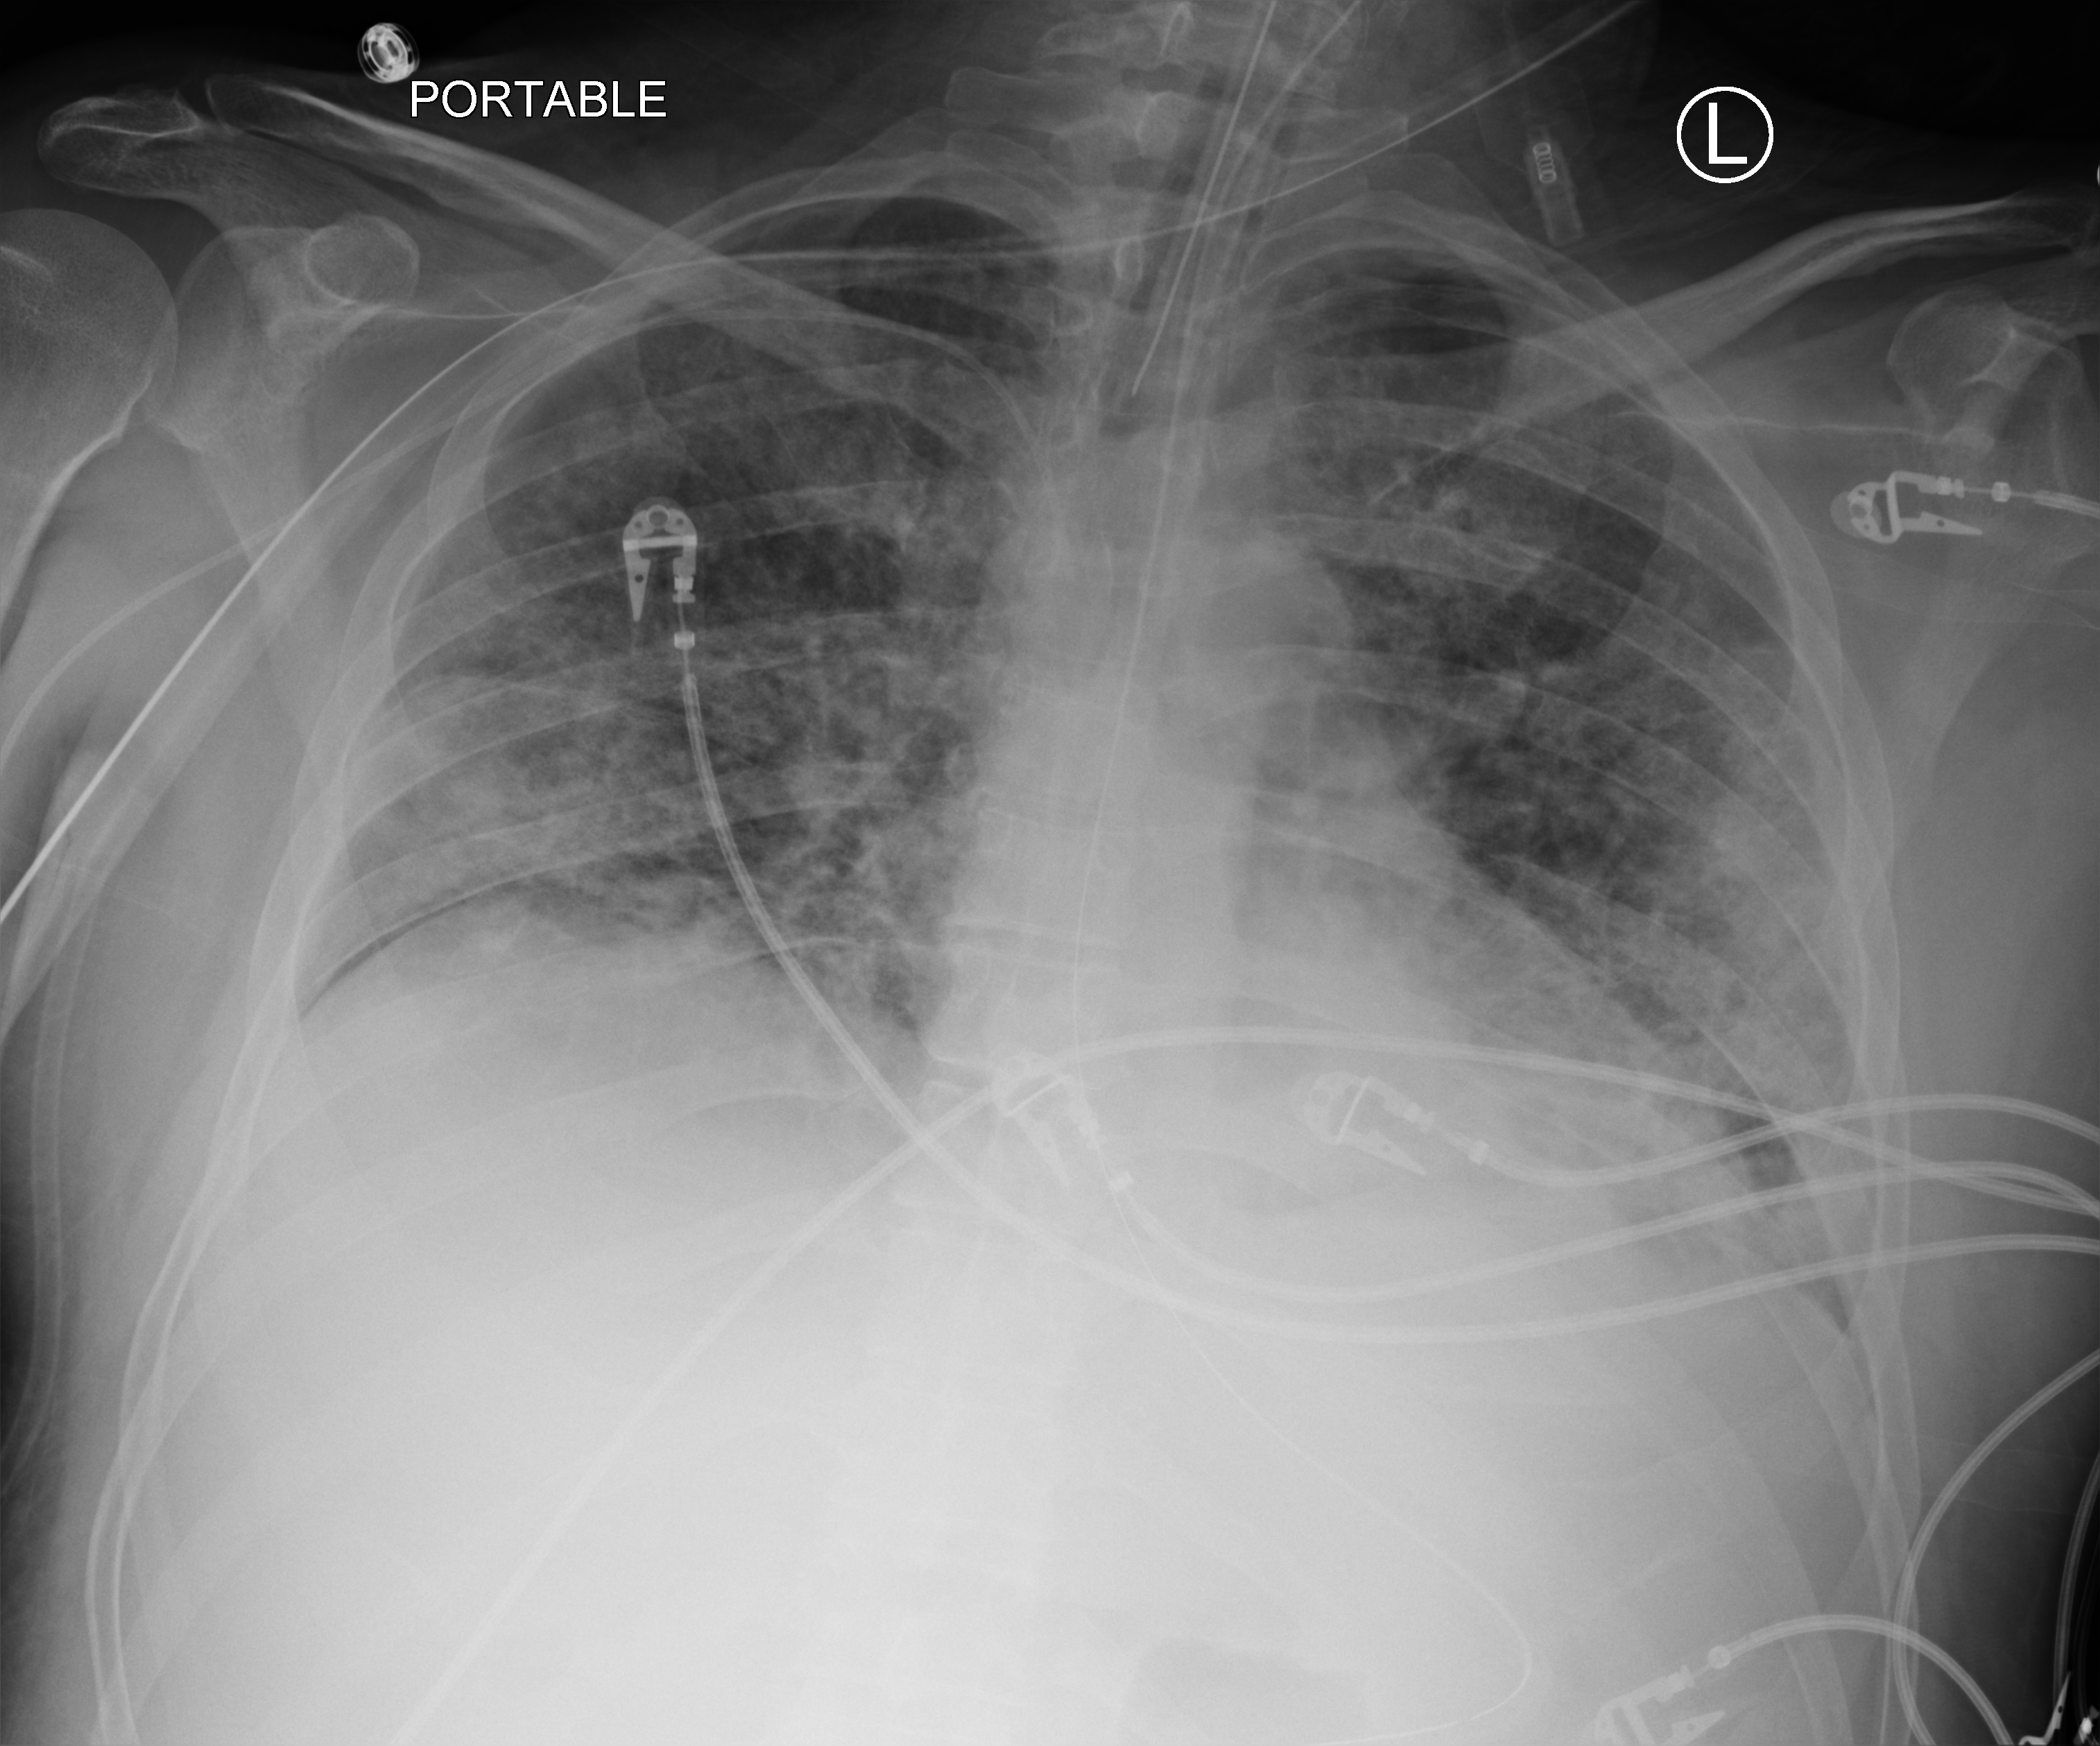
Chest X-ray (portable); anteroposterior (AP) projection. Patient hospitalised with COVID-19; male, aged 18–59 years.
From the hospital-stay record, not from the radiograph (when in the stay this image was taken is not recorded): chronic kidney disease (admission record): no; admitted to intensive care during this hospital stay: yes.